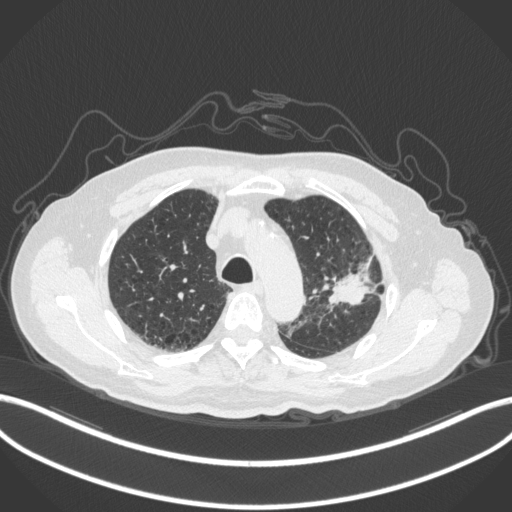
Chest CT, one axial slice; position 226 of 331 along the scan axis; 120 kVp; lung window (W 1500 / L -600 HU); 1 mm slice thickness; 512 × 512 image matrix, field of view 400 × 400 mm. Patient: male, 79 years. Case-level facts recorded for this patient, not image findings: clinical TNM (as recorded): T2a N1 M1.
Outlined on this slice (rectangle marked by the reading radiologist):
- lung tumour (recorded histology: adenocarcinoma): box from (x=324, y=247) to (x=384, y=308) px